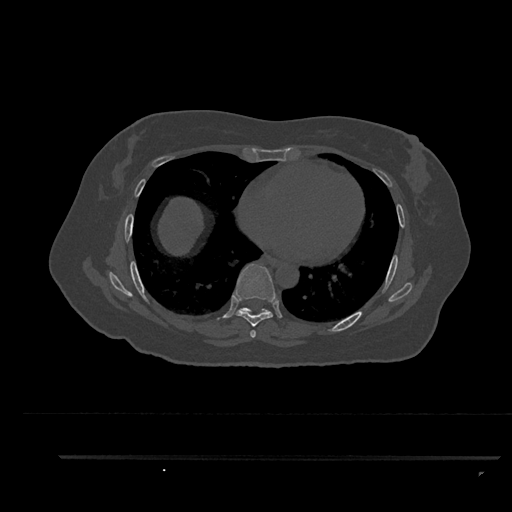
CT including the spine, one axial slice. Position 498 of 797 along the scan axis. Reconstruction kernel Br40s/3. 120 kVp. Bone window (W 1800 / L 400 HU). 0.5 mm slice thickness. 512 × 512 image matrix, field of view 408 × 408 mm. Female patient, age 44 years. Case-level facts recorded for this patient, not image findings: primary cancer: renal; vertebrae with lytic lesions (as recorded): L1.
Outlined on this slice (semi-automatic segmentation, software-assisted and operator-edited):
- T6 vertebra: bounding box <252,332,255,337> (left, top, right, bottom; pixels)
- T7 vertebra: <233,264,278,338>
- T8 vertebra: <236,308,269,315>